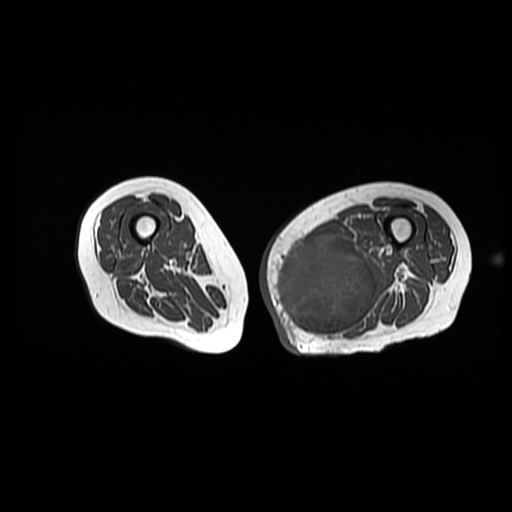
MRI of an extremity soft-tissue mass, one axial slice. Slice 32 of 42 in the series (ordered by position). 6 mm slice thickness. 512 × 512 image matrix. Female patient. From the clinical record (not read from this slice): histological type: pleomorphic leiomyosarcoma; grade: high; site of the primary tumour: left thigh.
Outlined on this slice (expert manual segmentation):
- gross tumour volume including surrounding oedema: box from (x=273, y=233) to (x=384, y=340) px
- gross tumour volume (mass): (x=273, y=233)–(x=378, y=338)